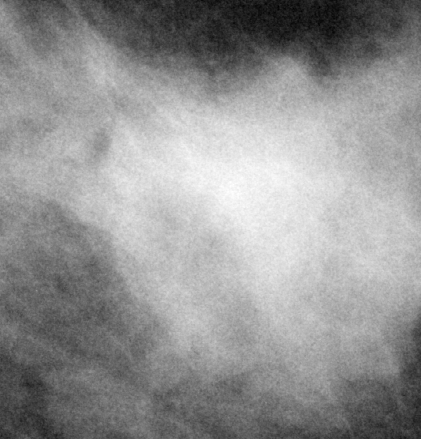
Cropped region of a digitized screen-film mammogram centred on a radiologist-marked abnormality, right breast, CC view, BI-RADS breast density category 3 (scale 1–4).
Finding: mass, shape irregular, margins microlobulated; BI-RADS assessment category 5; pathology (as recorded): malignant.